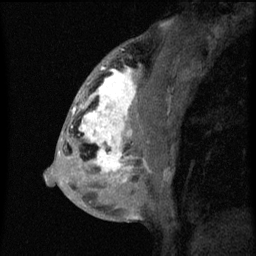
Breast MRI (dynamic contrast-enhanced), one sagittal slice; dynamic contrast-enhanced series, image 2 of 3 at this slice position (ordered by acquisition); 1.5 T; TE 4.2 ms, TR 8 ms; 2 mm slice thickness; 256 × 256 image matrix. Patient: female, 50 years.
Annotated regions visible in this slice (semi-automatically segmented with operator editing):
- analysis volume of interest (the breast-tissue region the enhancement analysis was run in; not a lesion): bounding box [x1, y1, x2, y2] px = [66, 64, 141, 187]
- tumour enhancement mask (voxels above the 70 % enhancement threshold inside the analysis volume of interest): [71, 66, 137, 183]